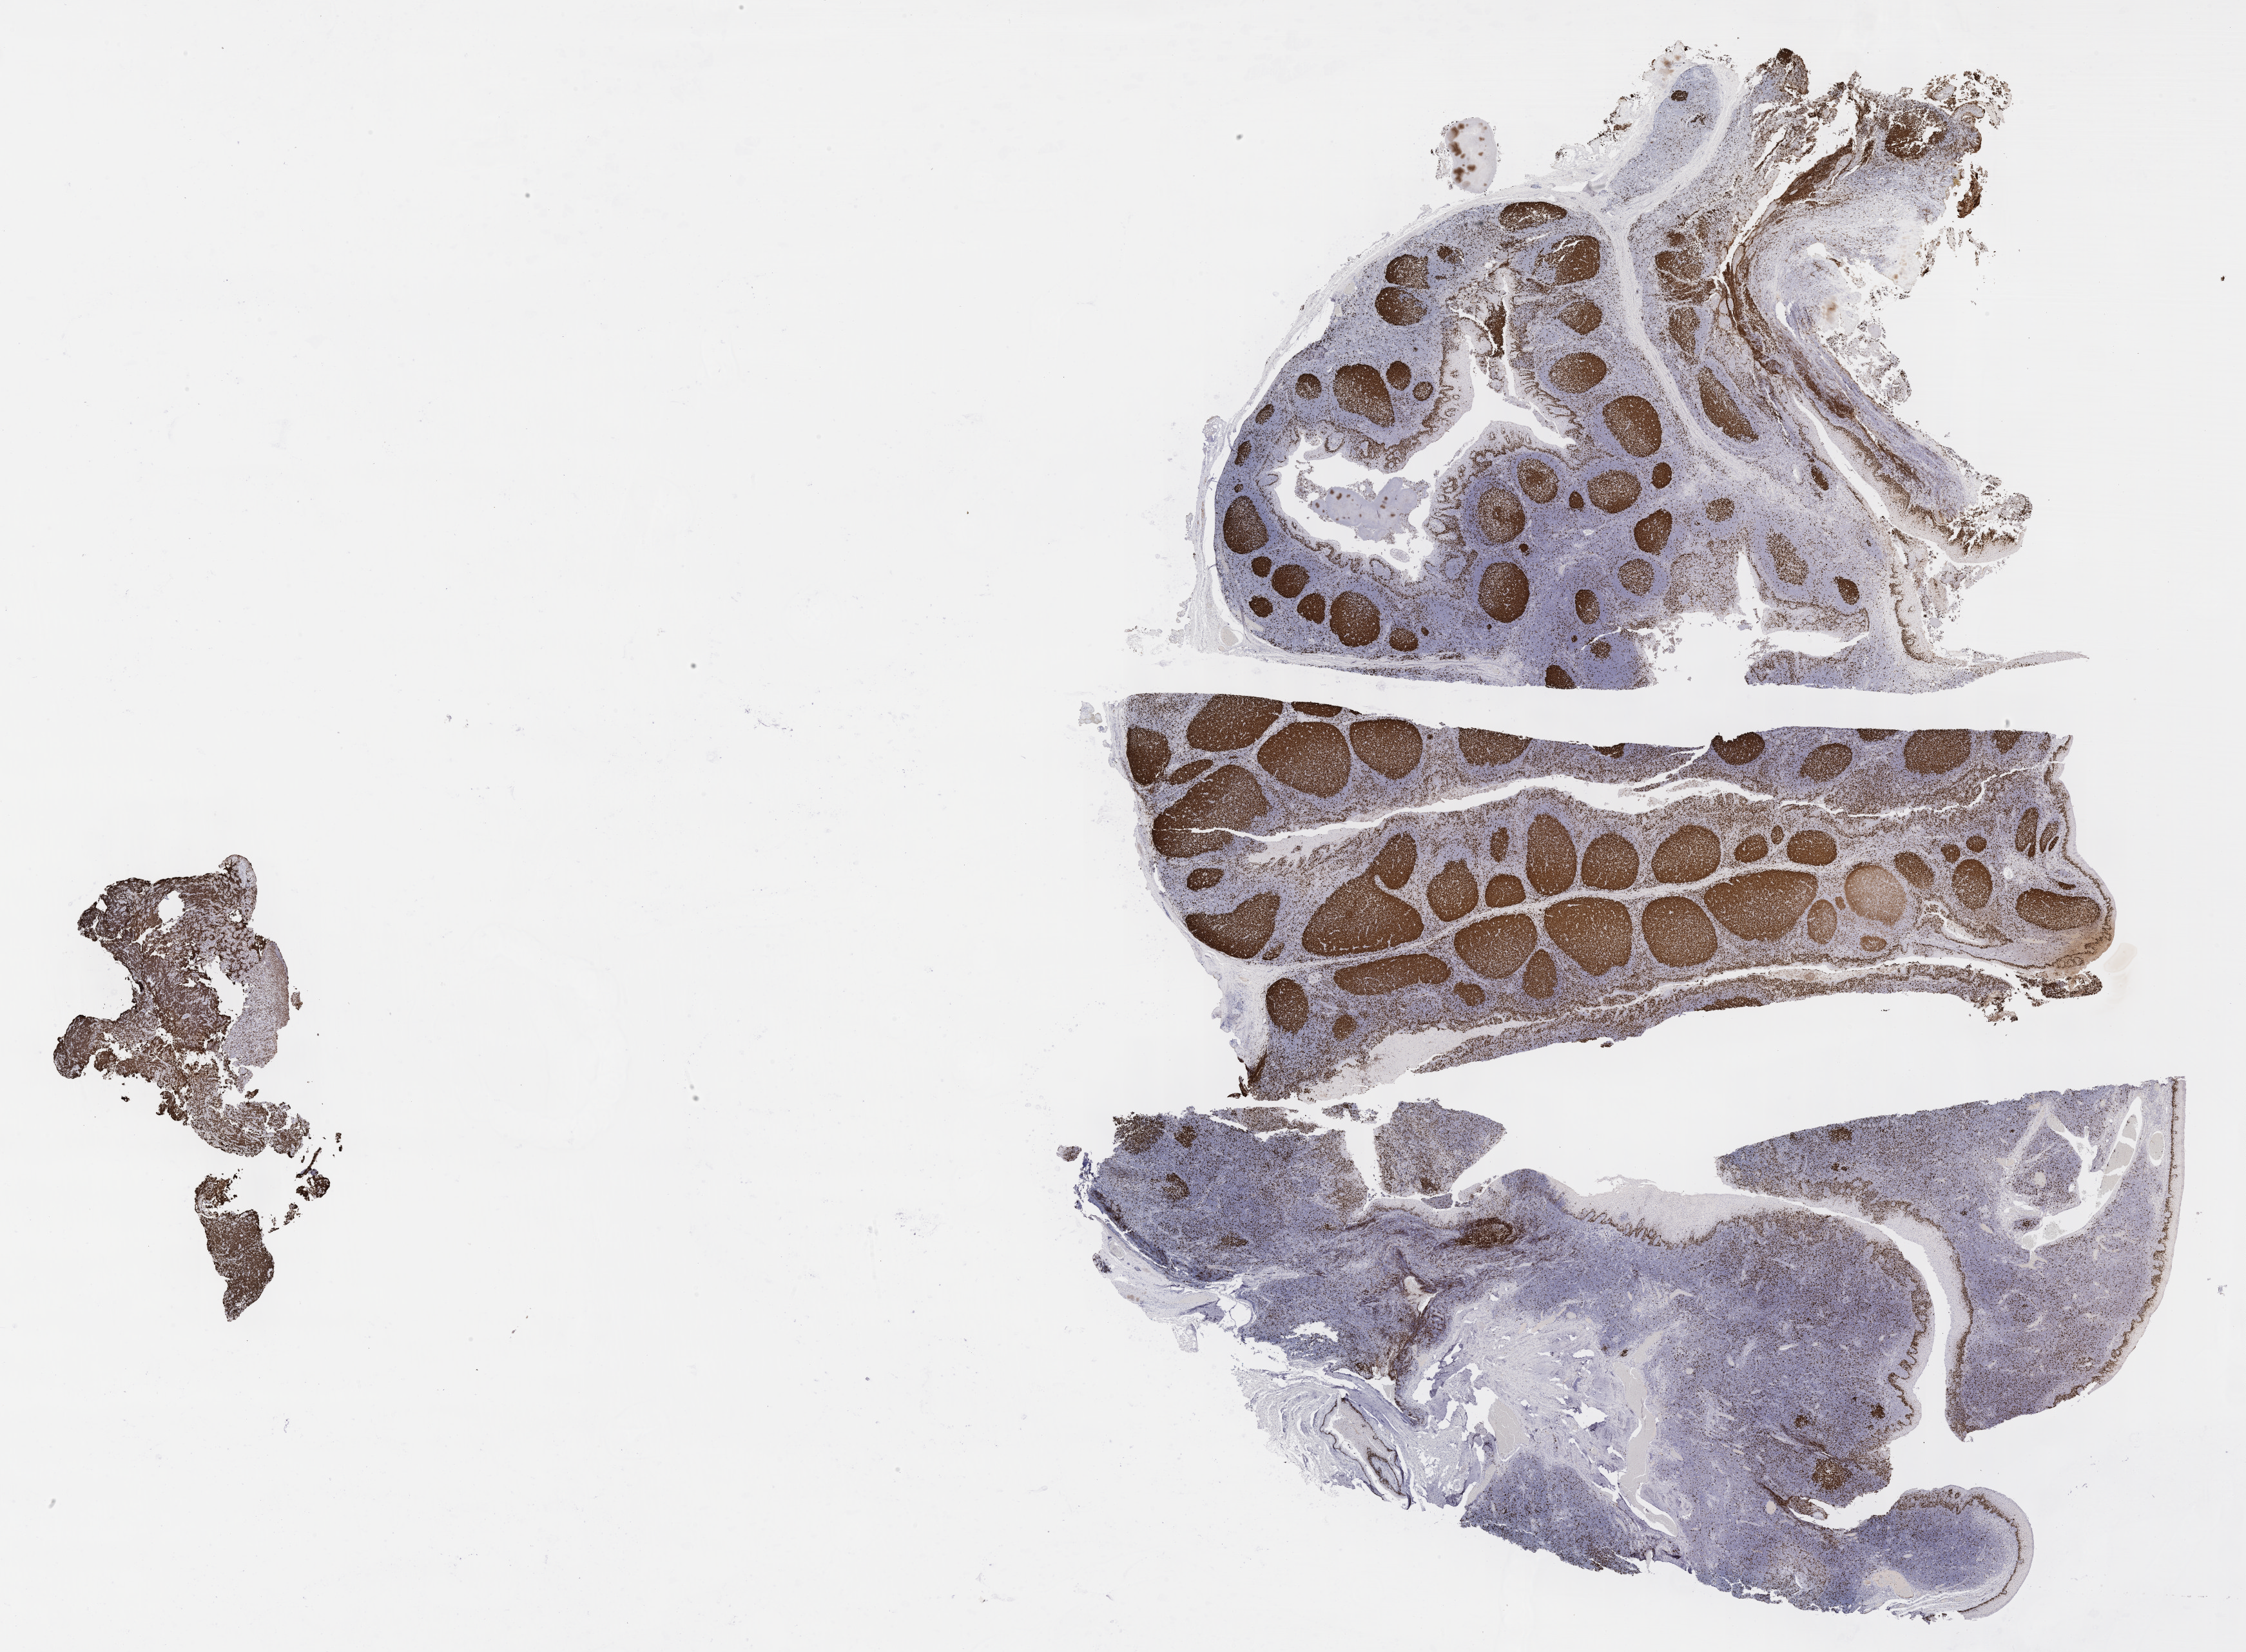
Immunohistochemistry (IHC) whole-slide image stained for Ki-67, a low-resolution overview of the entire scanned area, about 28.2 x 20.7 mm. Tumor tissue. Site: gum of mandible. Patient male; 10 years old.
Histologic diagnosis: Burkitt lymphoma, NOS.